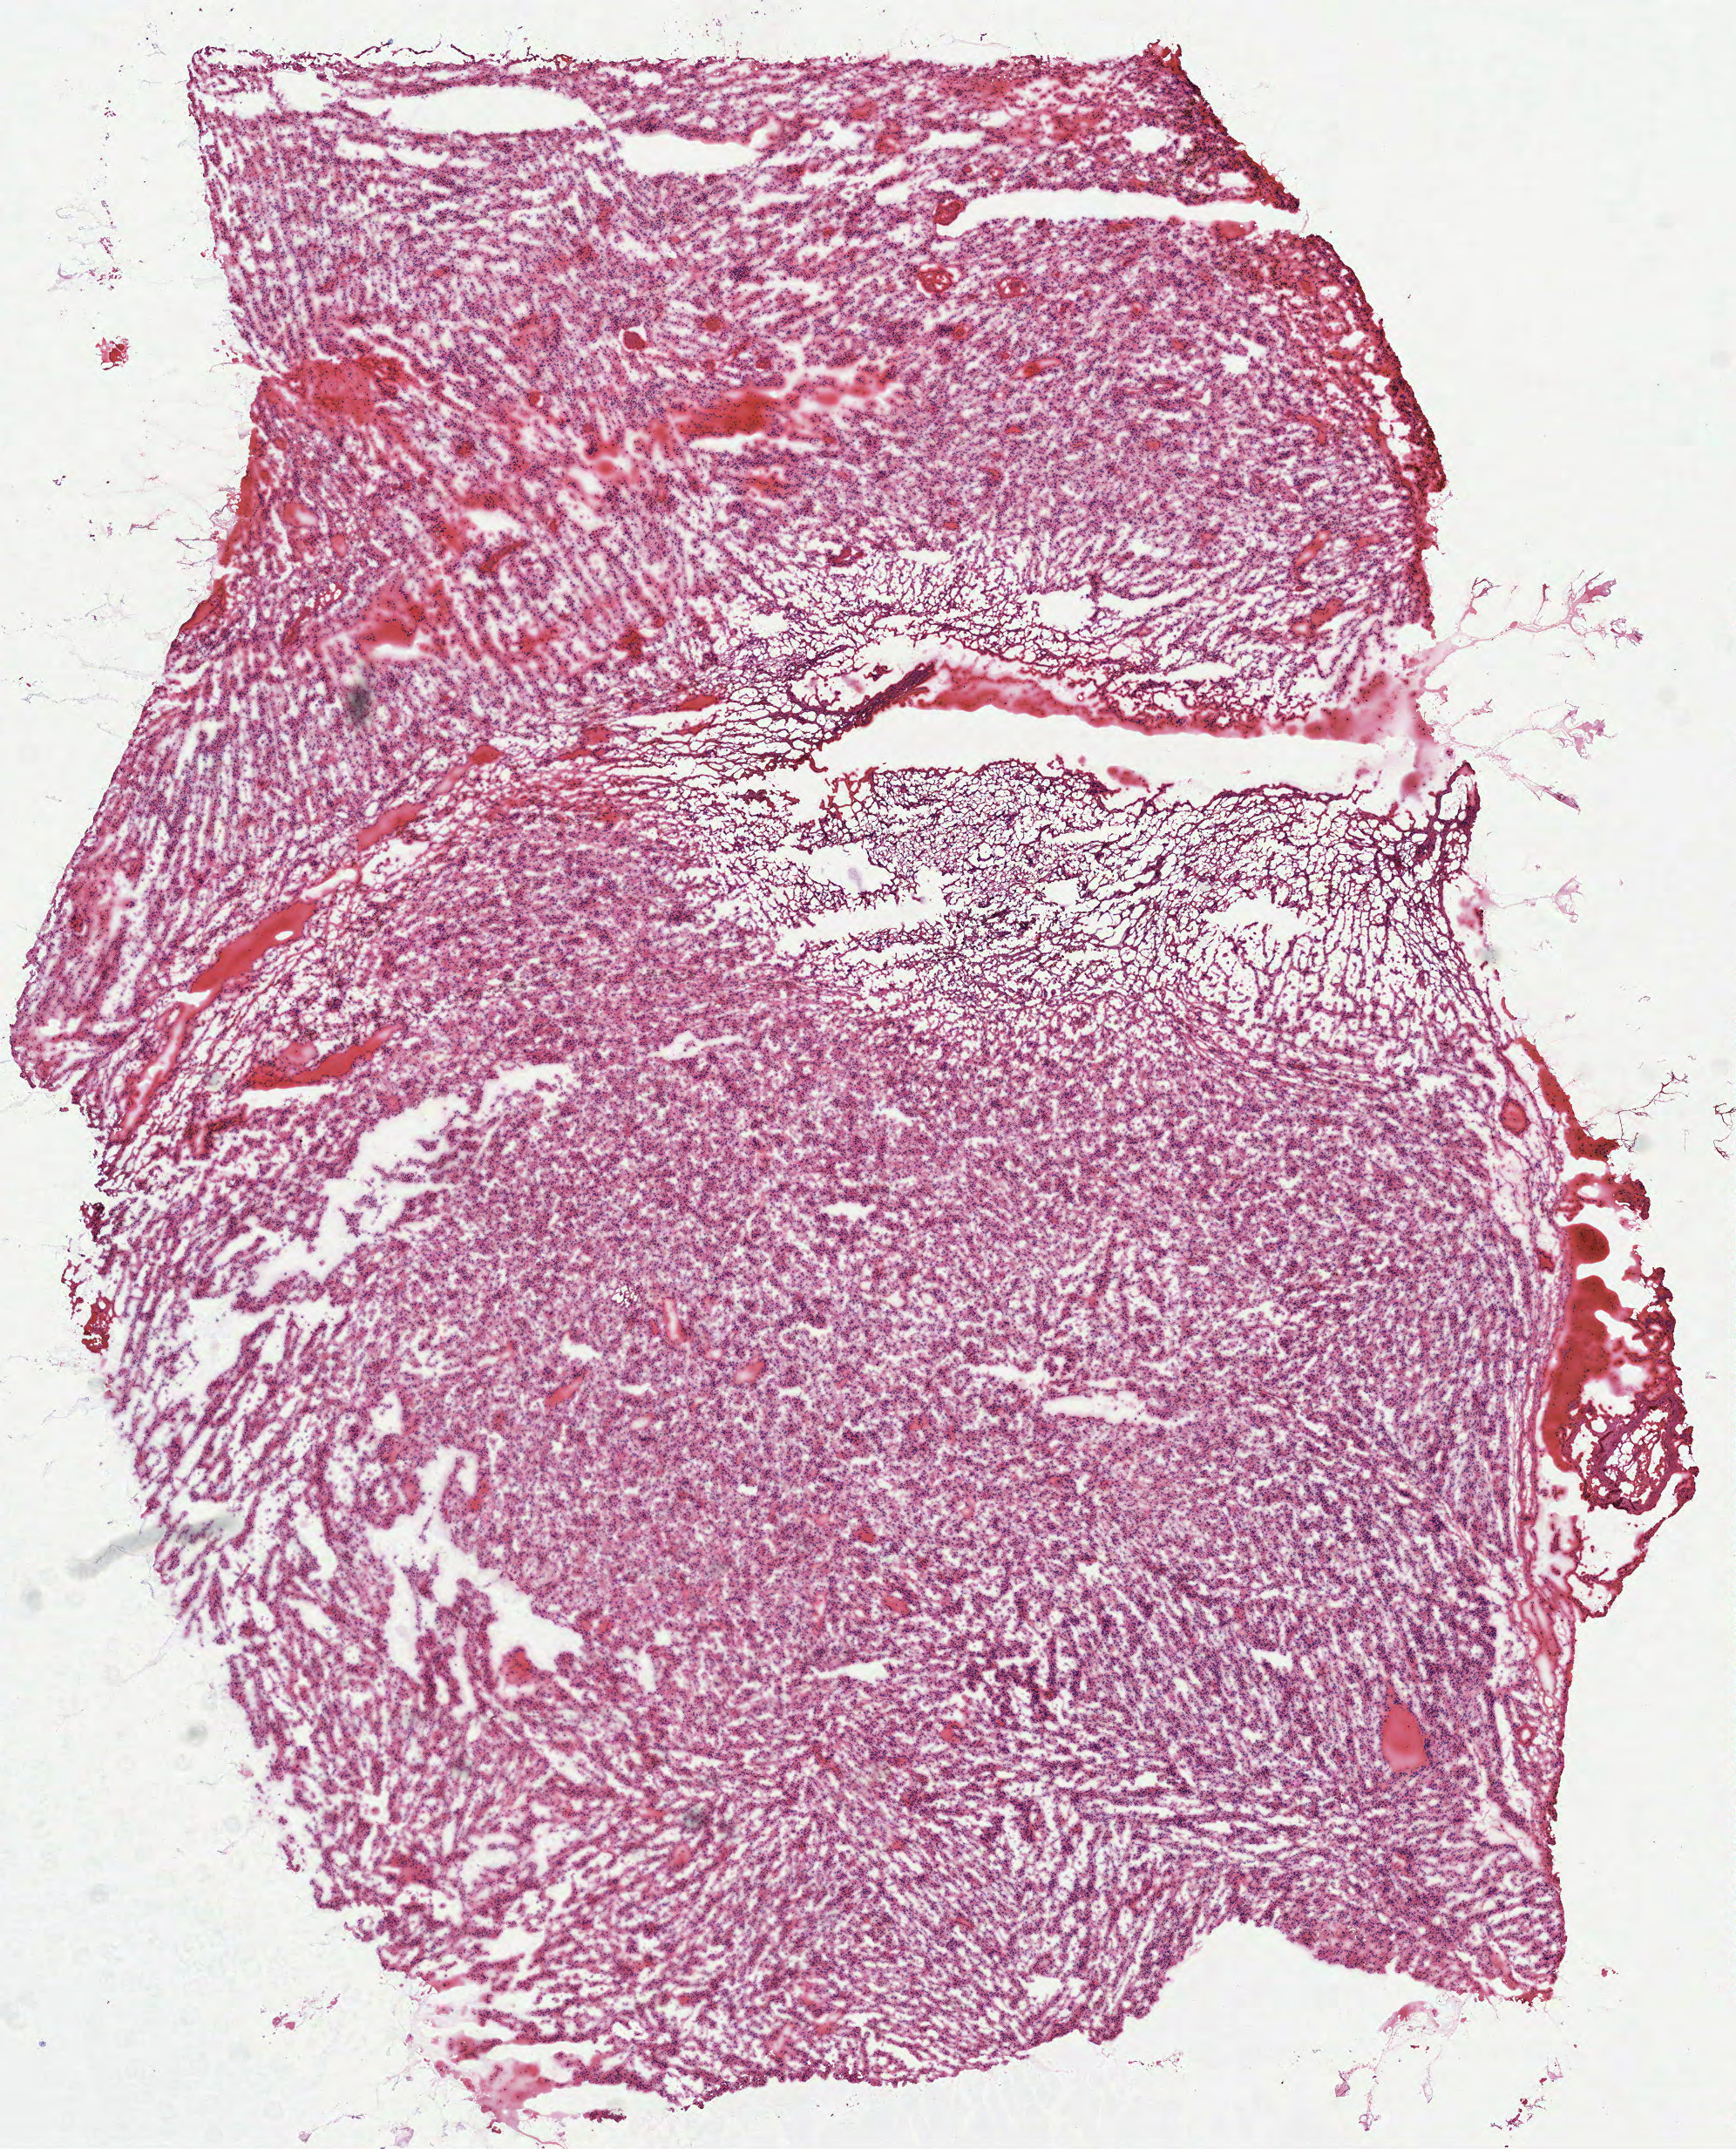
Digitized H&E-stained tissue section (whole slide), shown as a low-resolution overview of the whole scanned area (about 8.0 x 9.9 mm, acquisition: 40x scan); frozen section; brain, primary tumour sample. Female patient; age at initial diagnosis 49 years. Pathologist review of this section (percent, as recorded): tumour cells 100%, tumour nuclei 80%.
Diagnosis: Glioblastoma.